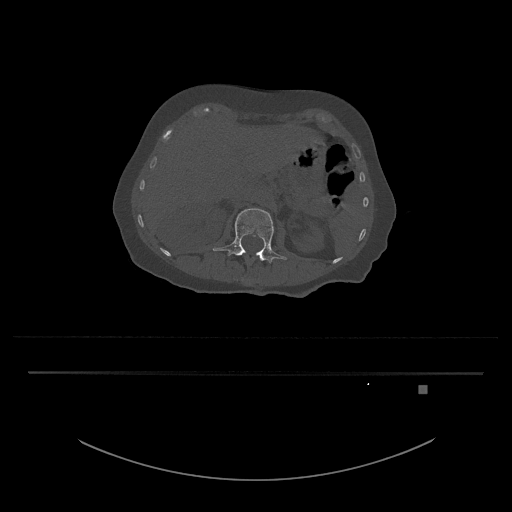
CT including the spine, one axial slice; reconstruction kernel Br40s/3; bone window (W 1800 / L 400 HU); 0.5 mm slice thickness; 512 × 512 image matrix, field of view 500 × 500 mm. Patient: female, 57 years. Case-level facts recorded for this patient, not image findings: primary cancer: cervical.
Annotated regions visible in this slice (semi-automatically segmented with operator editing):
- L1 vertebra: bounding box (x1, y1, x2, y2) in pixels: (245, 252, 264, 261)